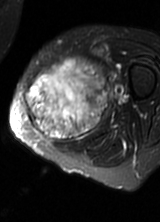
MRI of an extremity soft-tissue mass, one axial slice. Position 25 of 69 along the scan axis. T2-weighted fat-saturated. MR volume resampled by the dataset authors to the PET/CT grid (not the native acquisition matrix). 3.27 mm slice thickness. 160 × 222 image matrix, field of view 156 × 217 mm. Female patient. Case-level facts recorded for this patient, not image findings: histological type: pleomorphic leiomyosarcoma; grade: high; site of the primary tumour: left thigh.
Outlined on this slice (expert contour drawn on MRI and transferred to this co-registered scan by the dataset authors):
- gross tumour volume including surrounding oedema: bounding box (x1, y1, x2, y2) in pixels: (23, 59, 110, 142)
- gross tumour volume (mass): (23, 63, 108, 142)